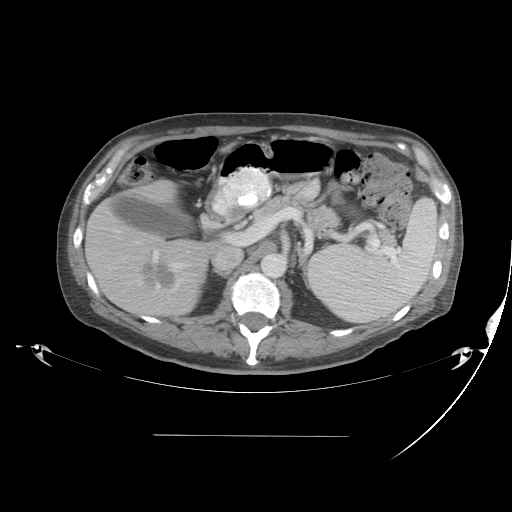
Contrast-enhanced abdominal CT, one axial slice. Position 24 of 48 along the scan axis. Reconstruction kernel STANDARD. 120 kVp. Intravenous contrast given. Soft-tissue window (W 400 / L 40 HU). 5 mm slice thickness. 512 × 512 image matrix. Male patient, age 65 years. Case-level facts recorded for this patient, not image findings: diagnosis: colorectal cancer liver metastases, imaged before liver resection; multiple liver metastases: yes; largest metastasis: 11 cm.
Outlined on this slice (manually delineated by an expert):
- hepatic veins: bounding box (x1, y1, x2, y2) in pixels: (99, 228, 186, 290)
- liver: (87, 181, 220, 317)
- planned liver remnant (the part of the liver to remain after resection): (135, 181, 180, 210)
- portal vein (with intrahepatic branches): (133, 235, 233, 261)
- liver metastasis: (144, 261, 176, 287)